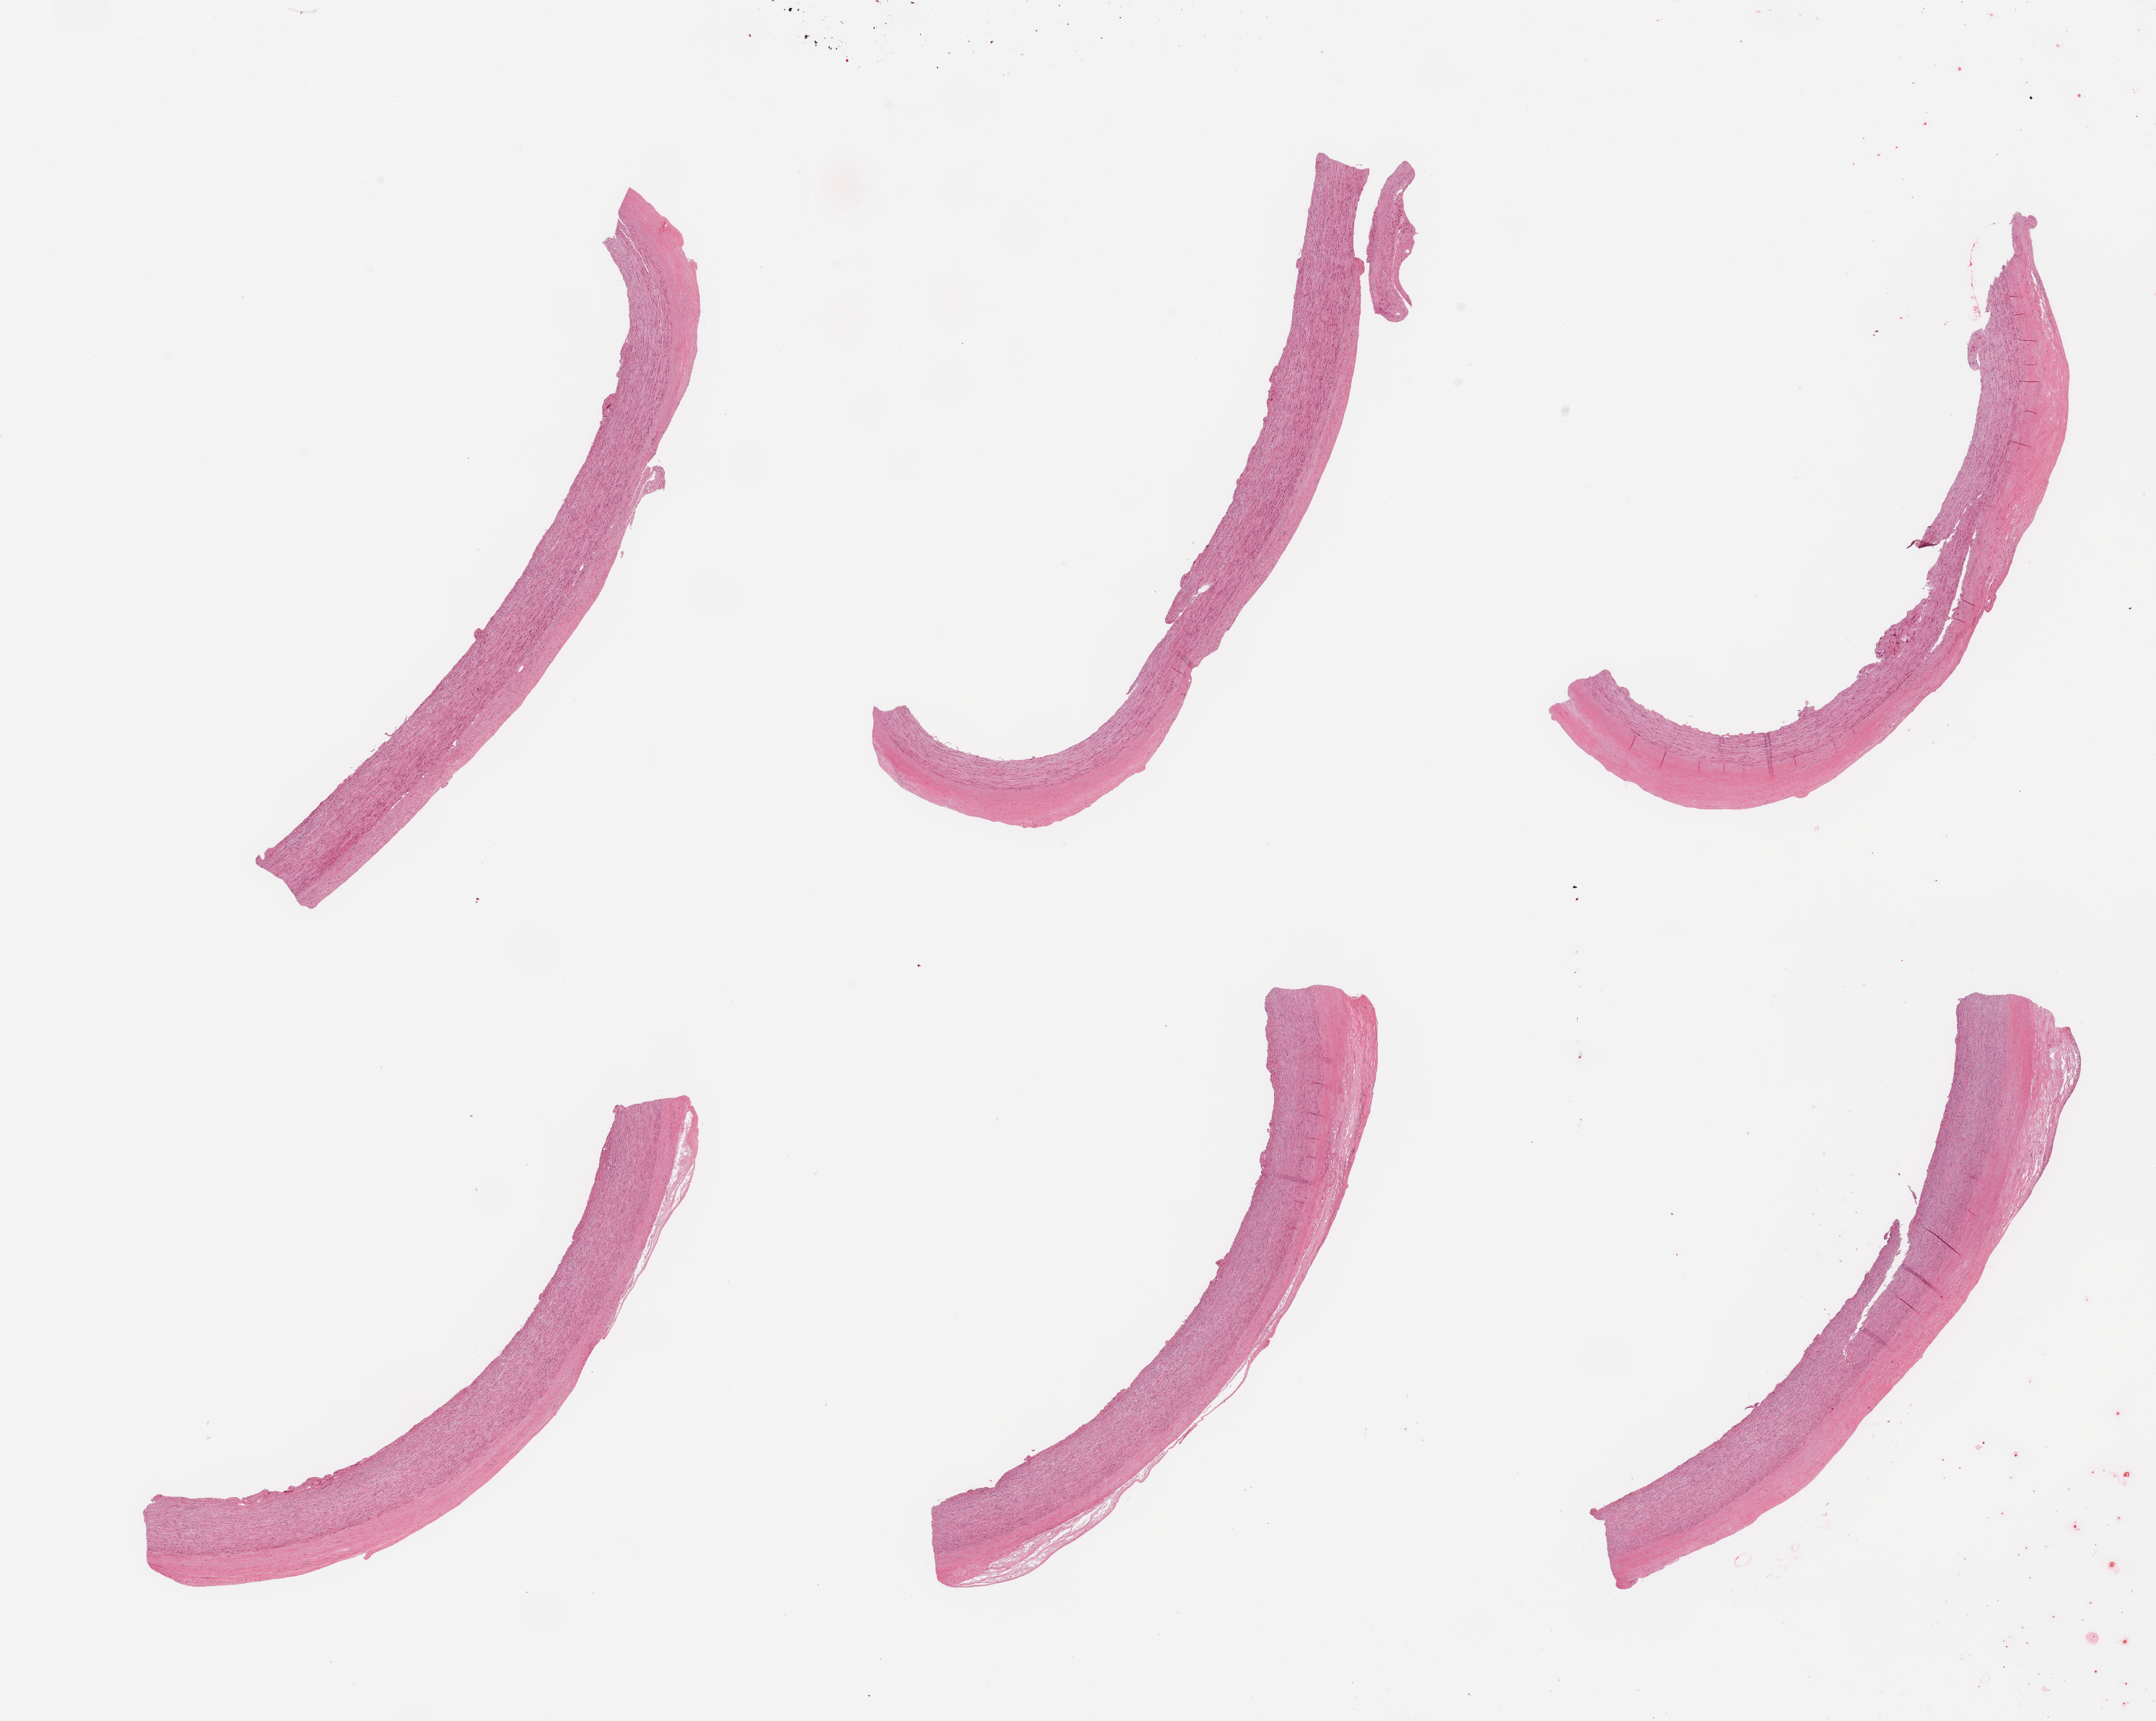
Digitized haematoxylin and eosin-stained section — a low-resolution overview of the entire scanned area, about 23.6 x 18.9 mm, PAXgene-fixed, paraffin-embedded tissue, section of aorta (target tissue), donor tissue sample. Donor sex: male.
- reviewer comment on this tissue sample: 6 pieces; mild flat plaques; well trimmed